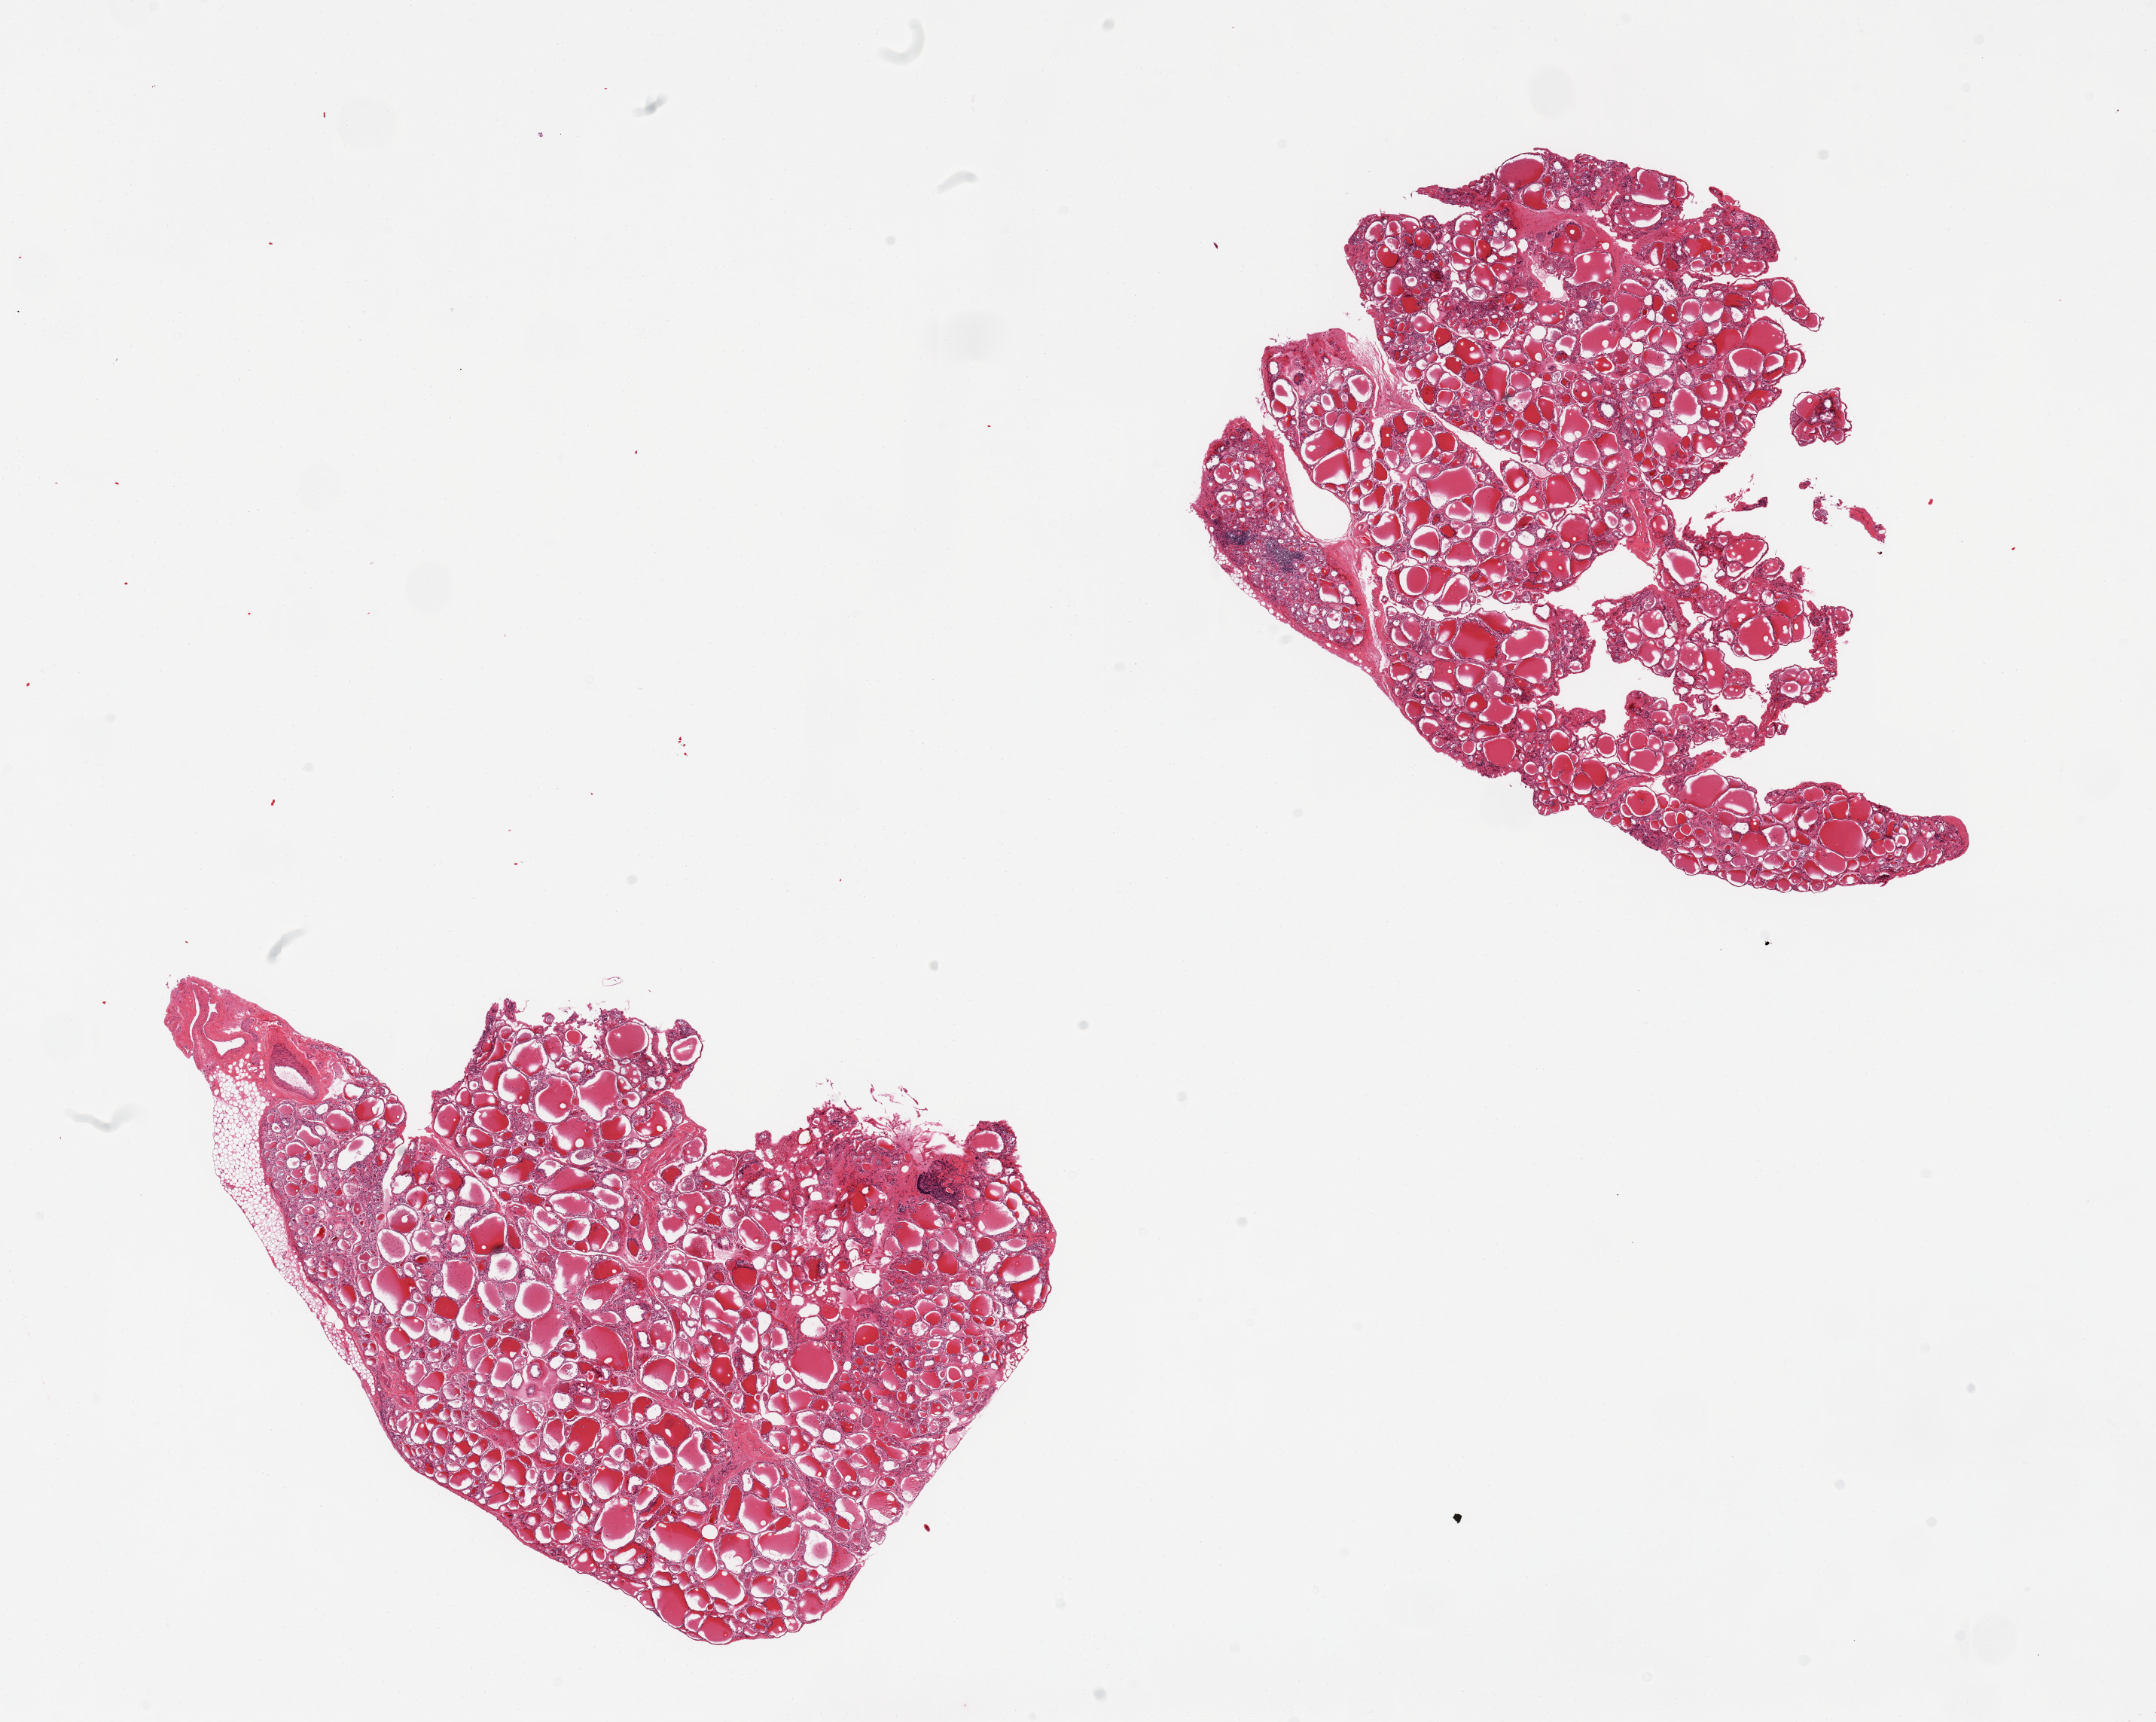
Whole-slide image, hematoxylin and eosin (H&E) stain — a low-resolution overview of the entire scanned area, about 22.6 x 18.1 mm (from a 20x scan), PAXgene-fixed, paraffin-embedded tissue, section of thyroid (target tissue), tissue donor sample. Male donor.
Pathologist's review note for this sample: 2 pieces, few collections of lymphocytes.